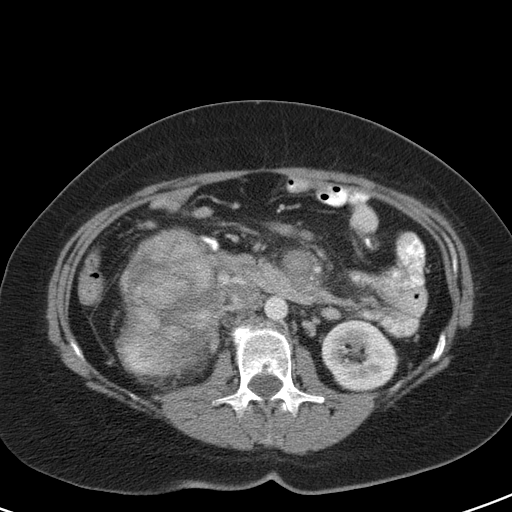
Contrast-enhanced abdominal CT, one axial slice; 120 kVp; intravenous contrast given; soft-tissue window (W 400 / L 40 HU); 5 mm slice thickness; 512 × 512 image matrix, field of view 356 × 356 mm. Female patient, age 51 years. Case-level facts recorded for this patient, not image findings: diagnosis: adrenocortical carcinoma; tumour side: right adrenal; tumour size at pathology: 17 cm; Ki-67 index: 12 %; stage (as recorded): 2.
Outlined on this slice (semi-automatically segmented with operator editing):
- mass: bounding box <121,233,216,366> (left, top, right, bottom; pixels)